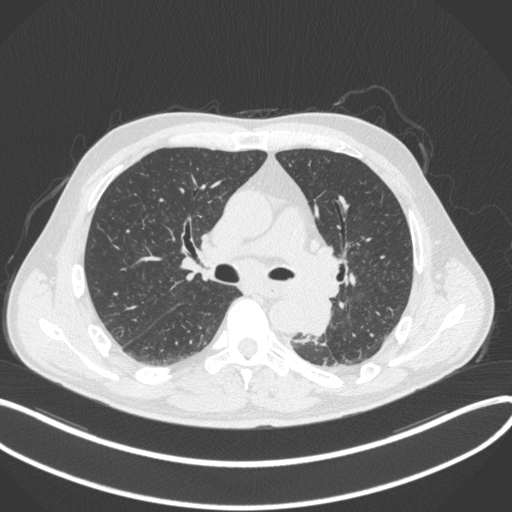
Chest CT, one axial slice. Position 207 of 328 along the scan axis. Reconstruction kernel B31f. 120 kVp. Lung window (W 1500 / L -600 HU). 1 mm slice thickness. 512 × 512 image matrix, field of view 400 × 400 mm. Male patient, age 59 years. From the clinical record (not read from this slice): clinical TNM (as recorded): T2a N2 M0.
Structures marked on this image (bounding box drawn by a radiologist):
- lung tumour (recorded histology: squamous cell carcinoma): bounding box (x1, y1, x2, y2) in pixels: (304, 290, 335, 336)